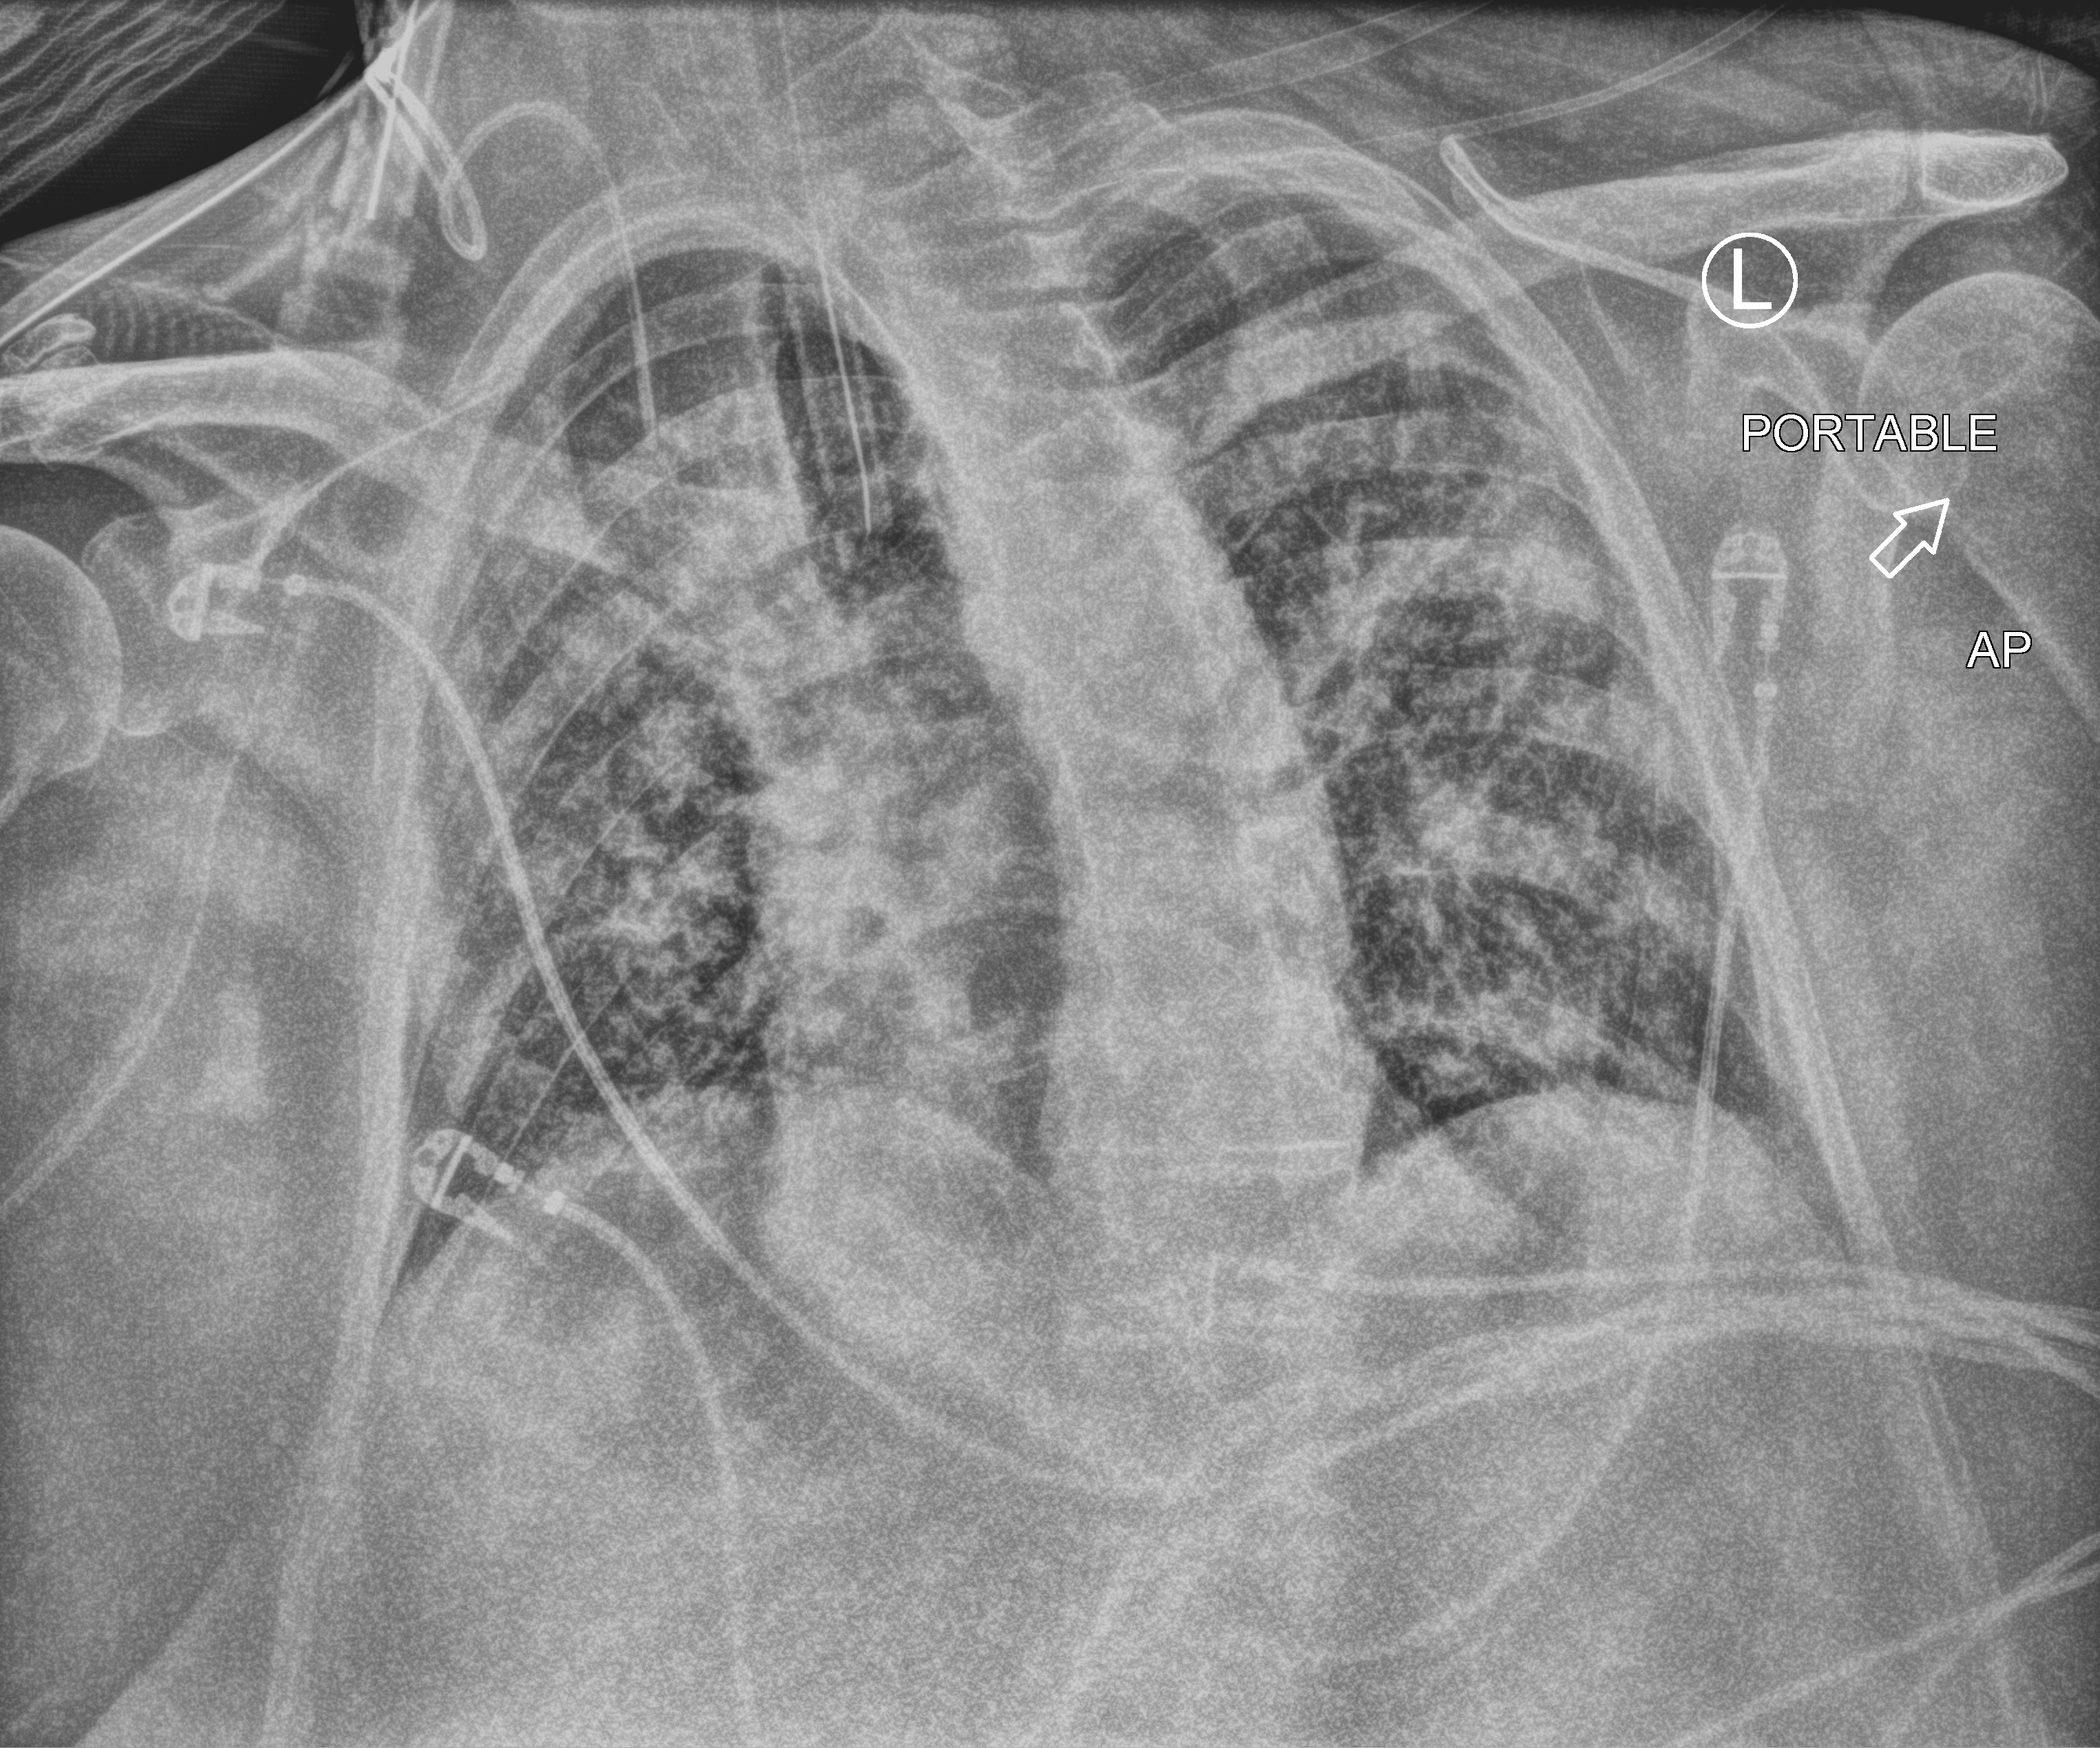
Chest X-ray (portable), anteroposterior (AP) projection. Patient hospitalised with COVID-19; male, aged 60–74 years.
Hospital-stay facts (about this admission, not read from this image; timing relative to this image not recorded): mechanically ventilated during this hospital stay: yes.